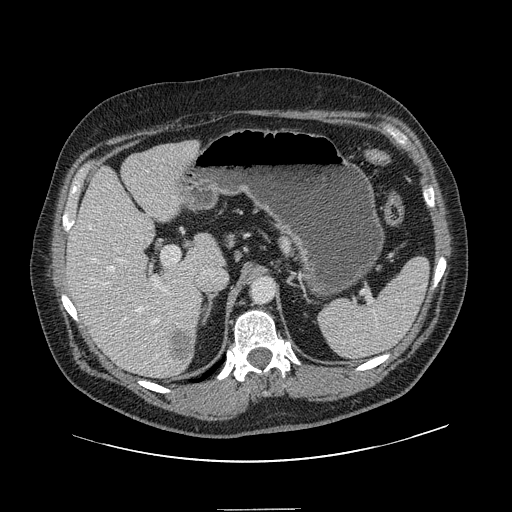
Contrast-enhanced abdominal CT, one axial slice. Slice 90 of 154 in the series (ordered by position). 120 kVp. Intravenous contrast given. Soft-tissue window (W 400 / L 40 HU). 512 × 512 image matrix, field of view 451 × 451 mm. Male patient, age 61 years. From the clinical record (not read from this slice): diagnosis: colorectal cancer liver metastases, imaged before liver resection; multiple liver metastases: yes; largest metastasis: 2.6 cm; disease in both lobes: yes.
Annotated regions visible in this slice (manually delineated by an expert):
- hepatic veins: bounding box [x1, y1, x2, y2] px = [89, 226, 159, 360]
- liver: [68, 142, 221, 377]
- planned liver remnant (the part of the liver to remain after resection): [68, 147, 222, 365]
- portal vein (with intrahepatic branches): [104, 259, 166, 291]
- liver metastasis: [171, 332, 195, 364]